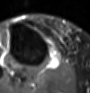
MRI of an extremity soft-tissue mass, one axial slice. Position 42 of 60 along the scan axis. STIR. MR volume resampled by the dataset authors to the PET/CT grid (not the native acquisition matrix). 3.27 mm slice thickness. 90 × 93 image matrix, field of view 88 × 91 mm. Female patient. Case-level facts recorded for this patient, not image findings: histological type: undifferentiated – high grade; grade: high; site of the primary tumour: right thigh.
Annotated regions visible in this slice (expert contour drawn on MRI and transferred to this co-registered scan by the dataset authors):
- gross tumour volume (mass): bounding box (x1, y1, x2, y2) in pixels: (49, 55, 59, 68)